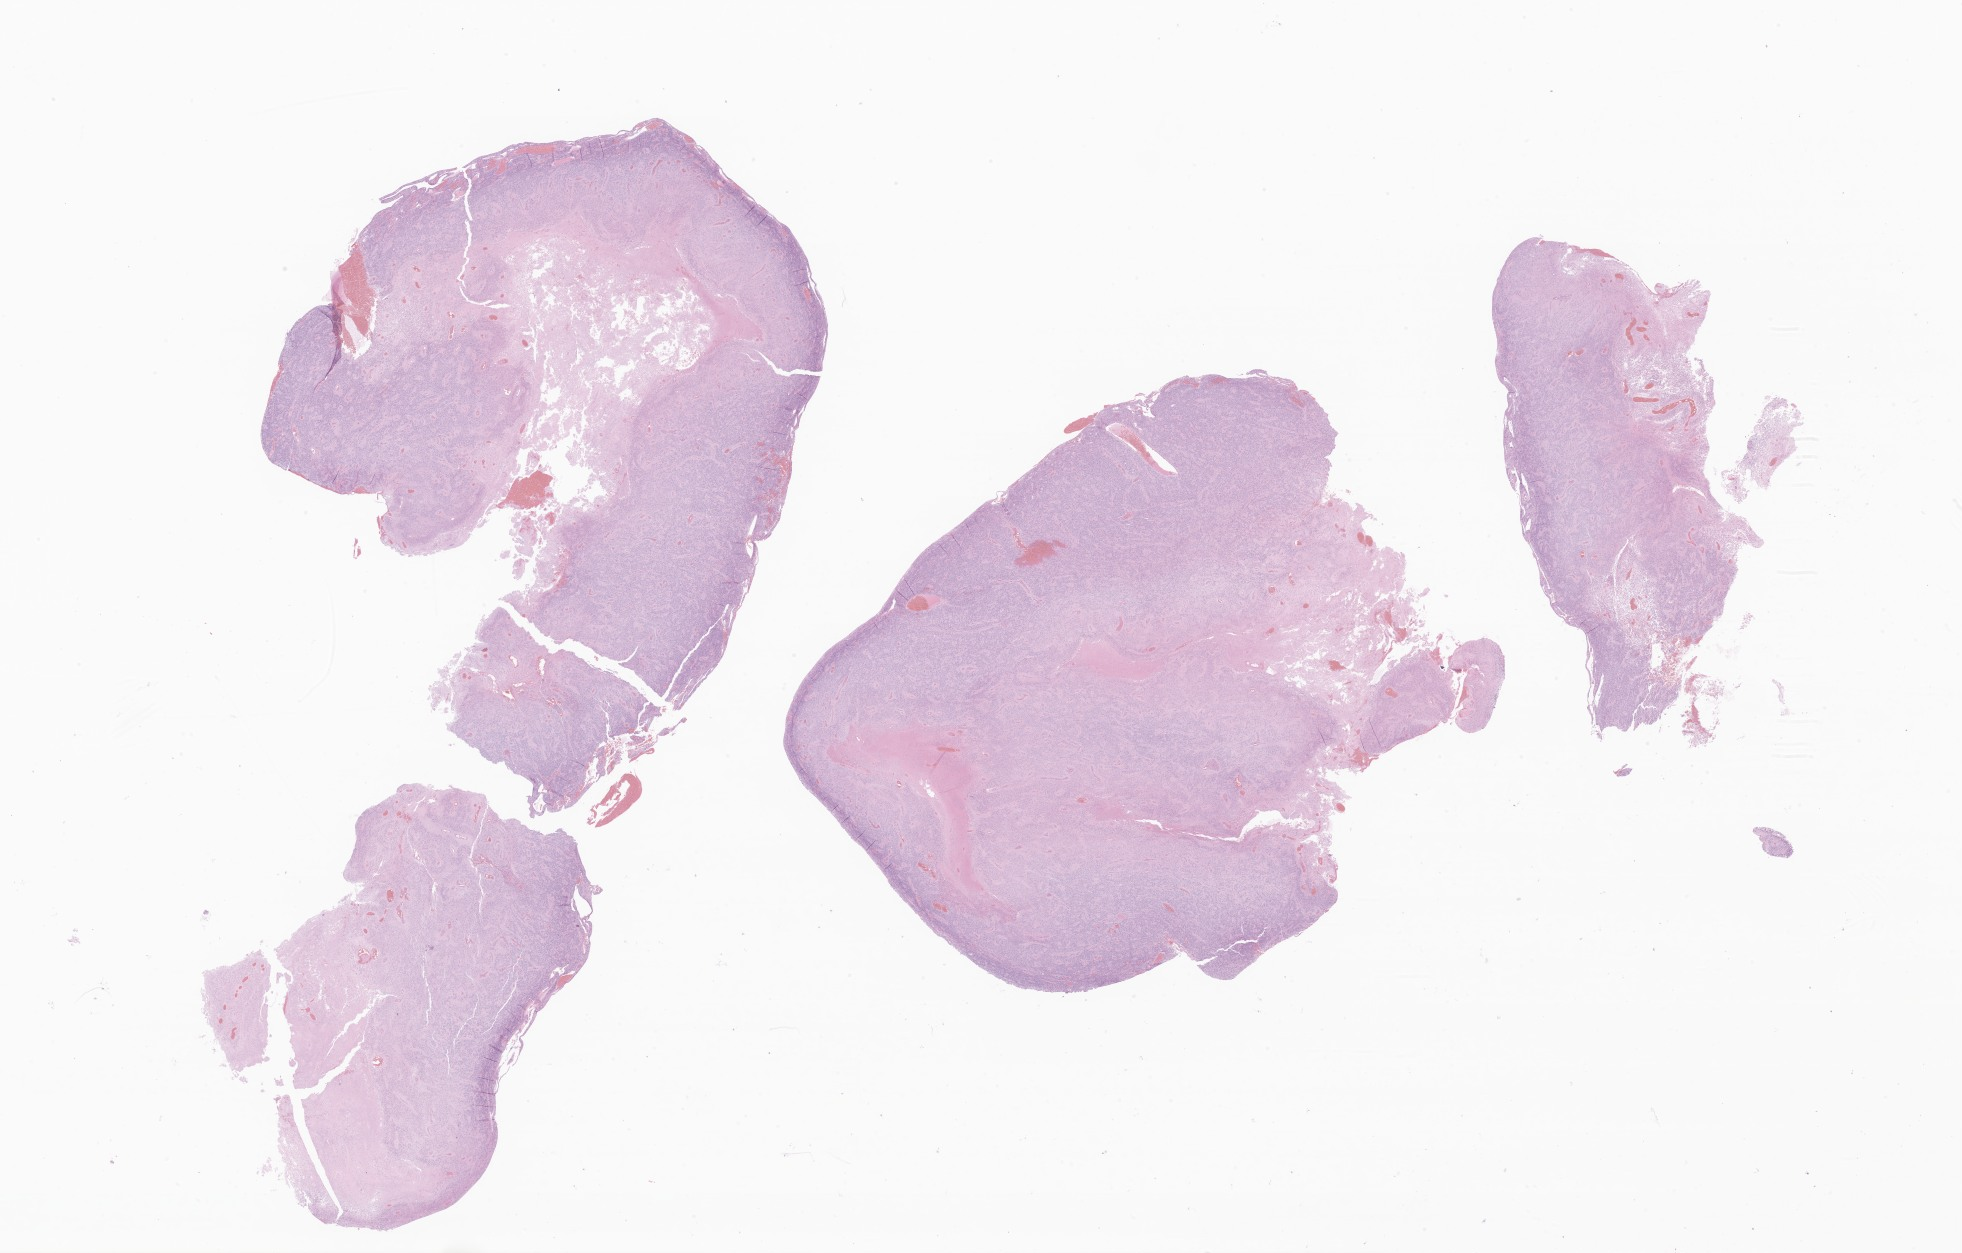
Digitized H&E-stained section of tumor tissue from the brain, shown as a low-resolution overview of the whole scanned area (about 33.1 x 21.1 mm). Formalin-fixed paraffin-embedded section. Patient: female, age 44 months.
- diagnosis (ICD-O-3 morphology term): Ependymoma, NOS